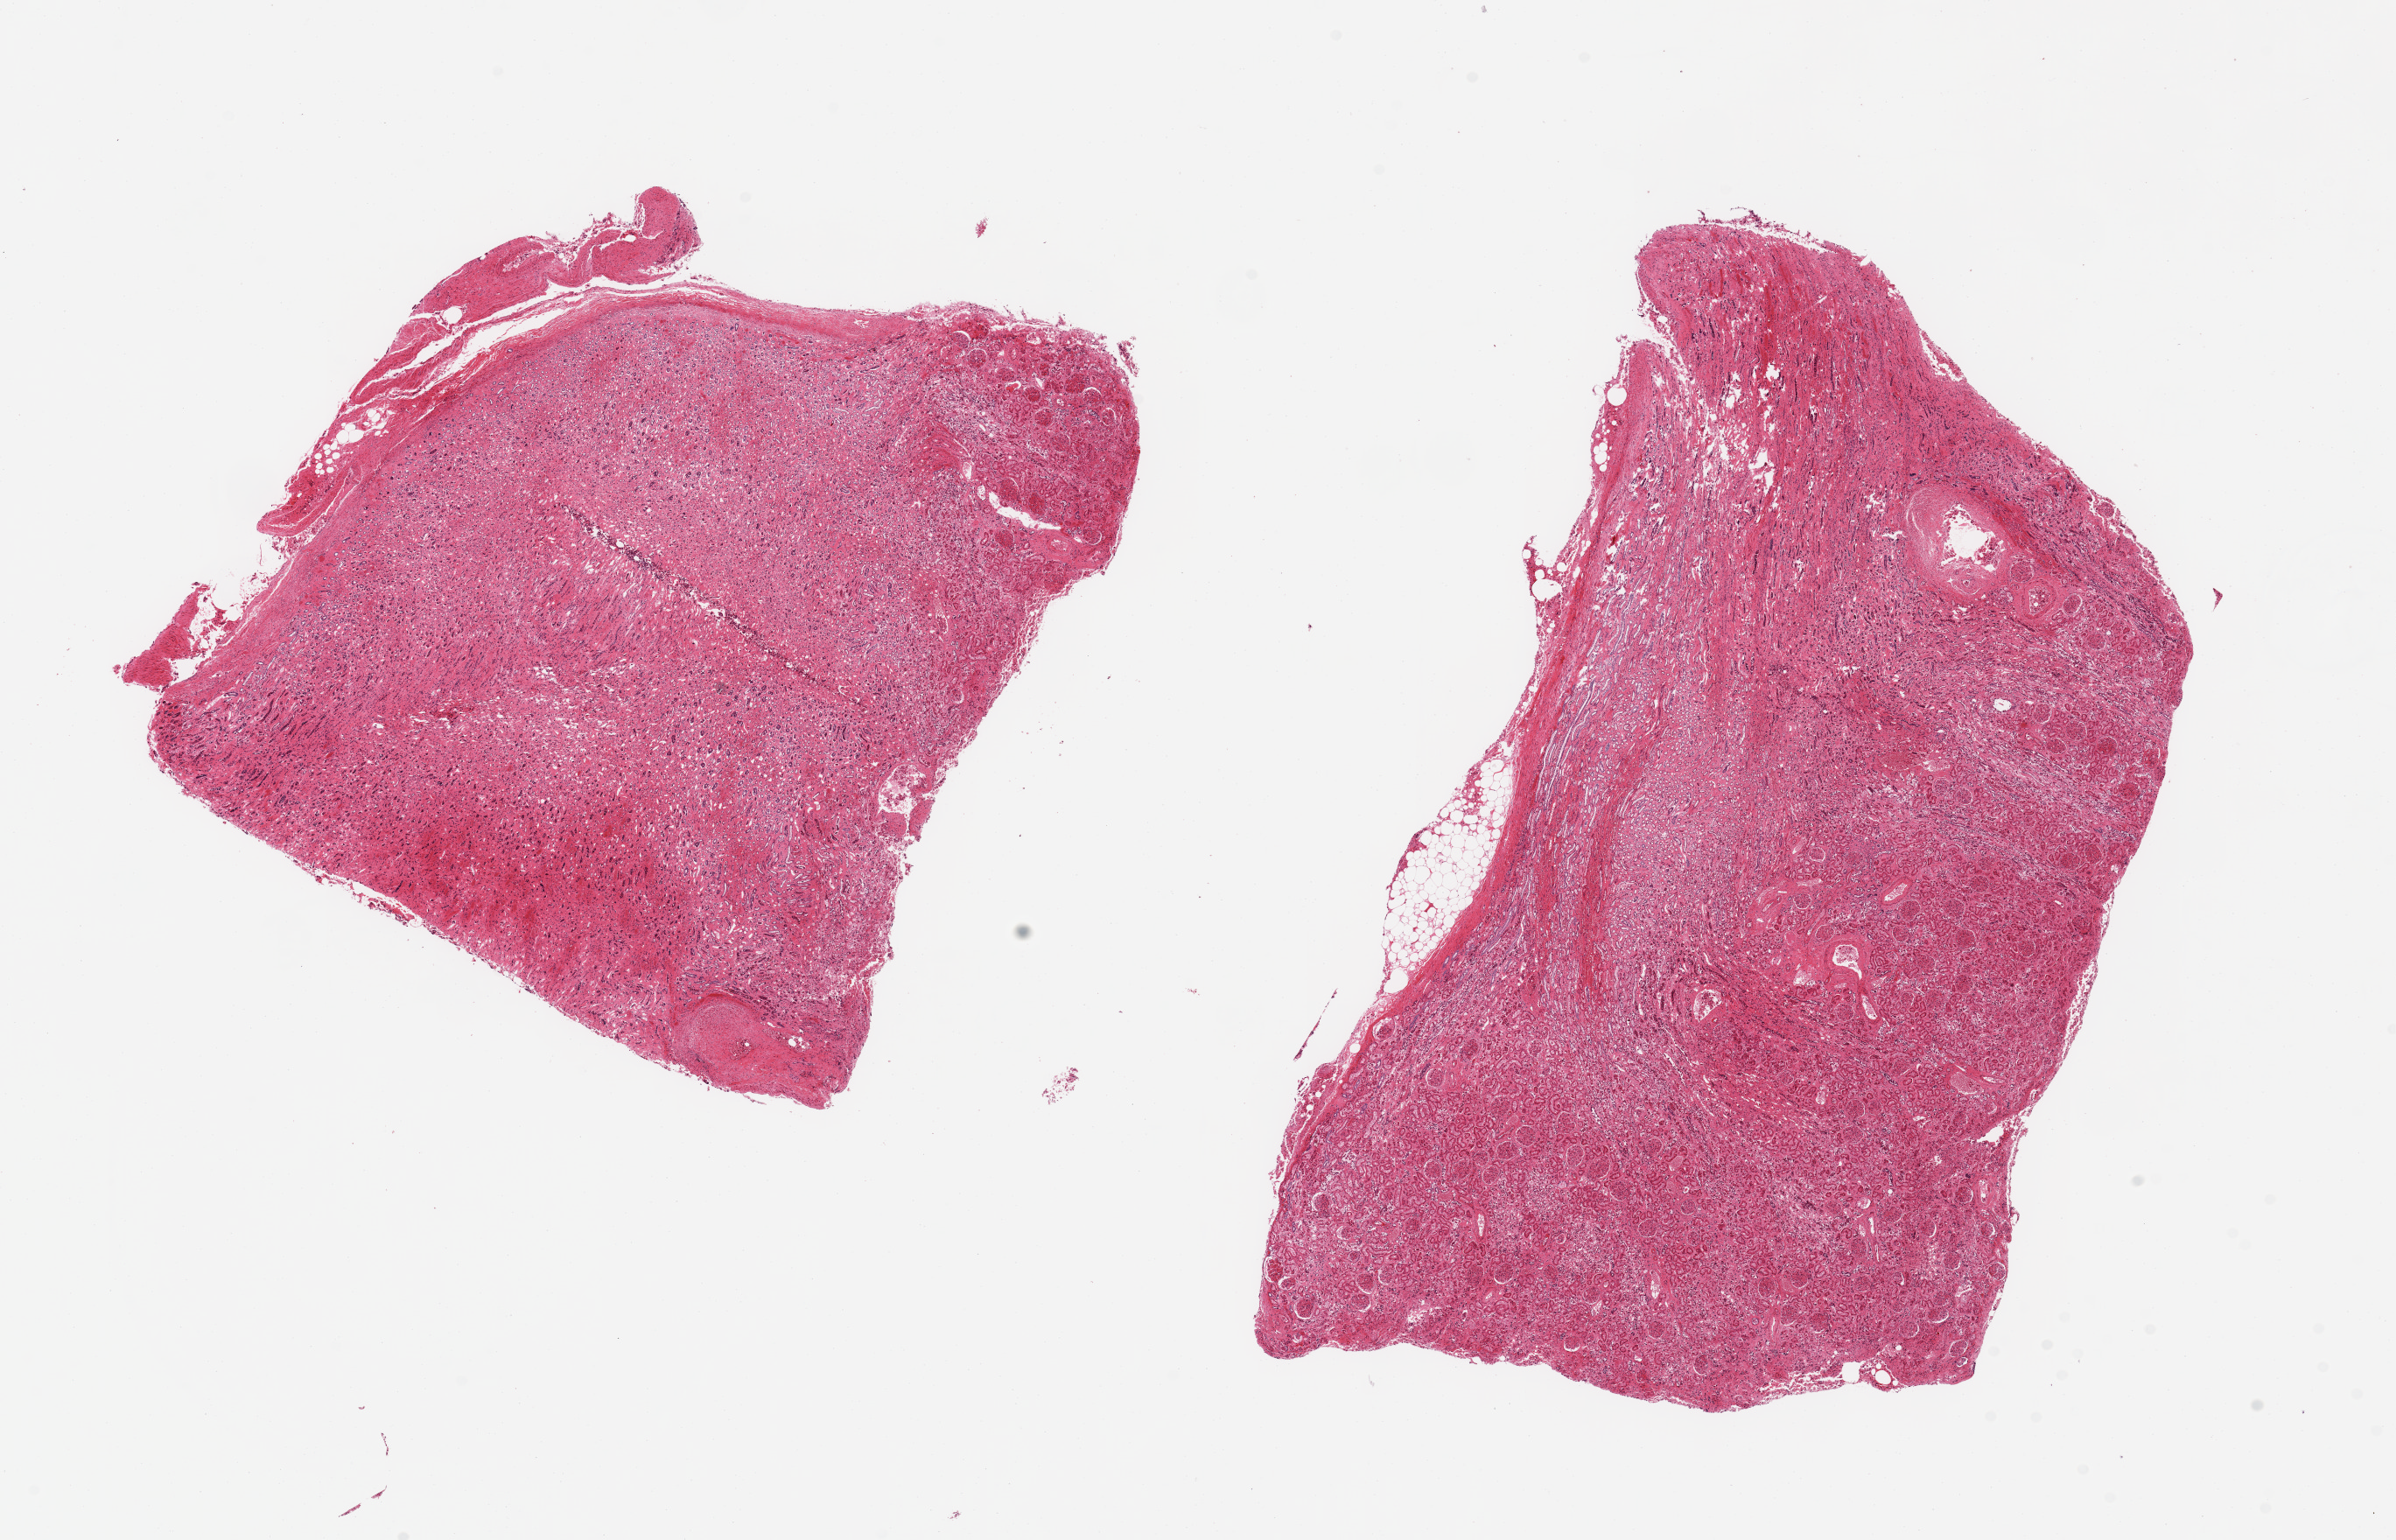
Digitized haematoxylin and eosin-stained section, brightfield — a low-resolution overview of the entire scanned area, about 21.7 x 13.9 mm, PAXgene-fixed paraffin-embedded (PFPE) section, target tissue: renal medulla, tissue donor sample. Male donor.
Pathologist's review note for this sample: 2 pieces,~11x6 mm half cortex; one piece 6x7mm 10% cortex; collecting ducts severely autolyzed.